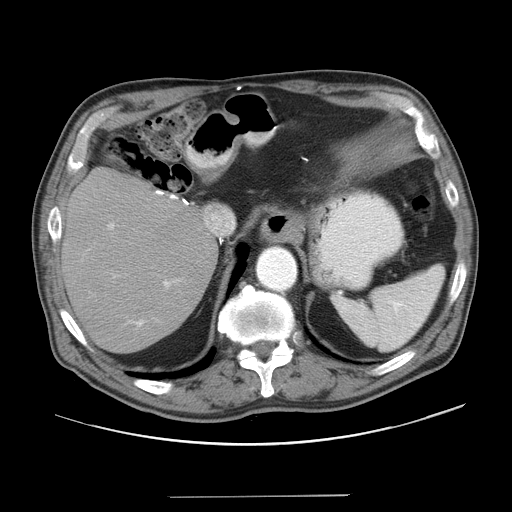
Contrast-enhanced abdominal CT, one axial slice; slice 31 of 41 in the series (ordered by position); reconstruction kernel STANDARD; 120 kVp; intravenous contrast given; soft-tissue window (W 400 / L 40 HU); 512 × 512 image matrix, field of view 420 × 420 mm. Male patient, age 75 years. Case-level facts recorded for this patient, not image findings: diagnosis: colorectal cancer liver metastases, imaged before liver resection; multiple liver metastases: no; largest metastasis: 5.2 cm; disease in both lobes: no.
Annotated regions visible in this slice (expert manual segmentation):
- hepatic veins: bounding box <204,207,236,238> (left, top, right, bottom; pixels)
- liver: <64,170,216,353>
- planned liver remnant (the part of the liver to remain after resection): <75,207,216,354>
- portal vein (with intrahepatic branches): <107,222,181,327>